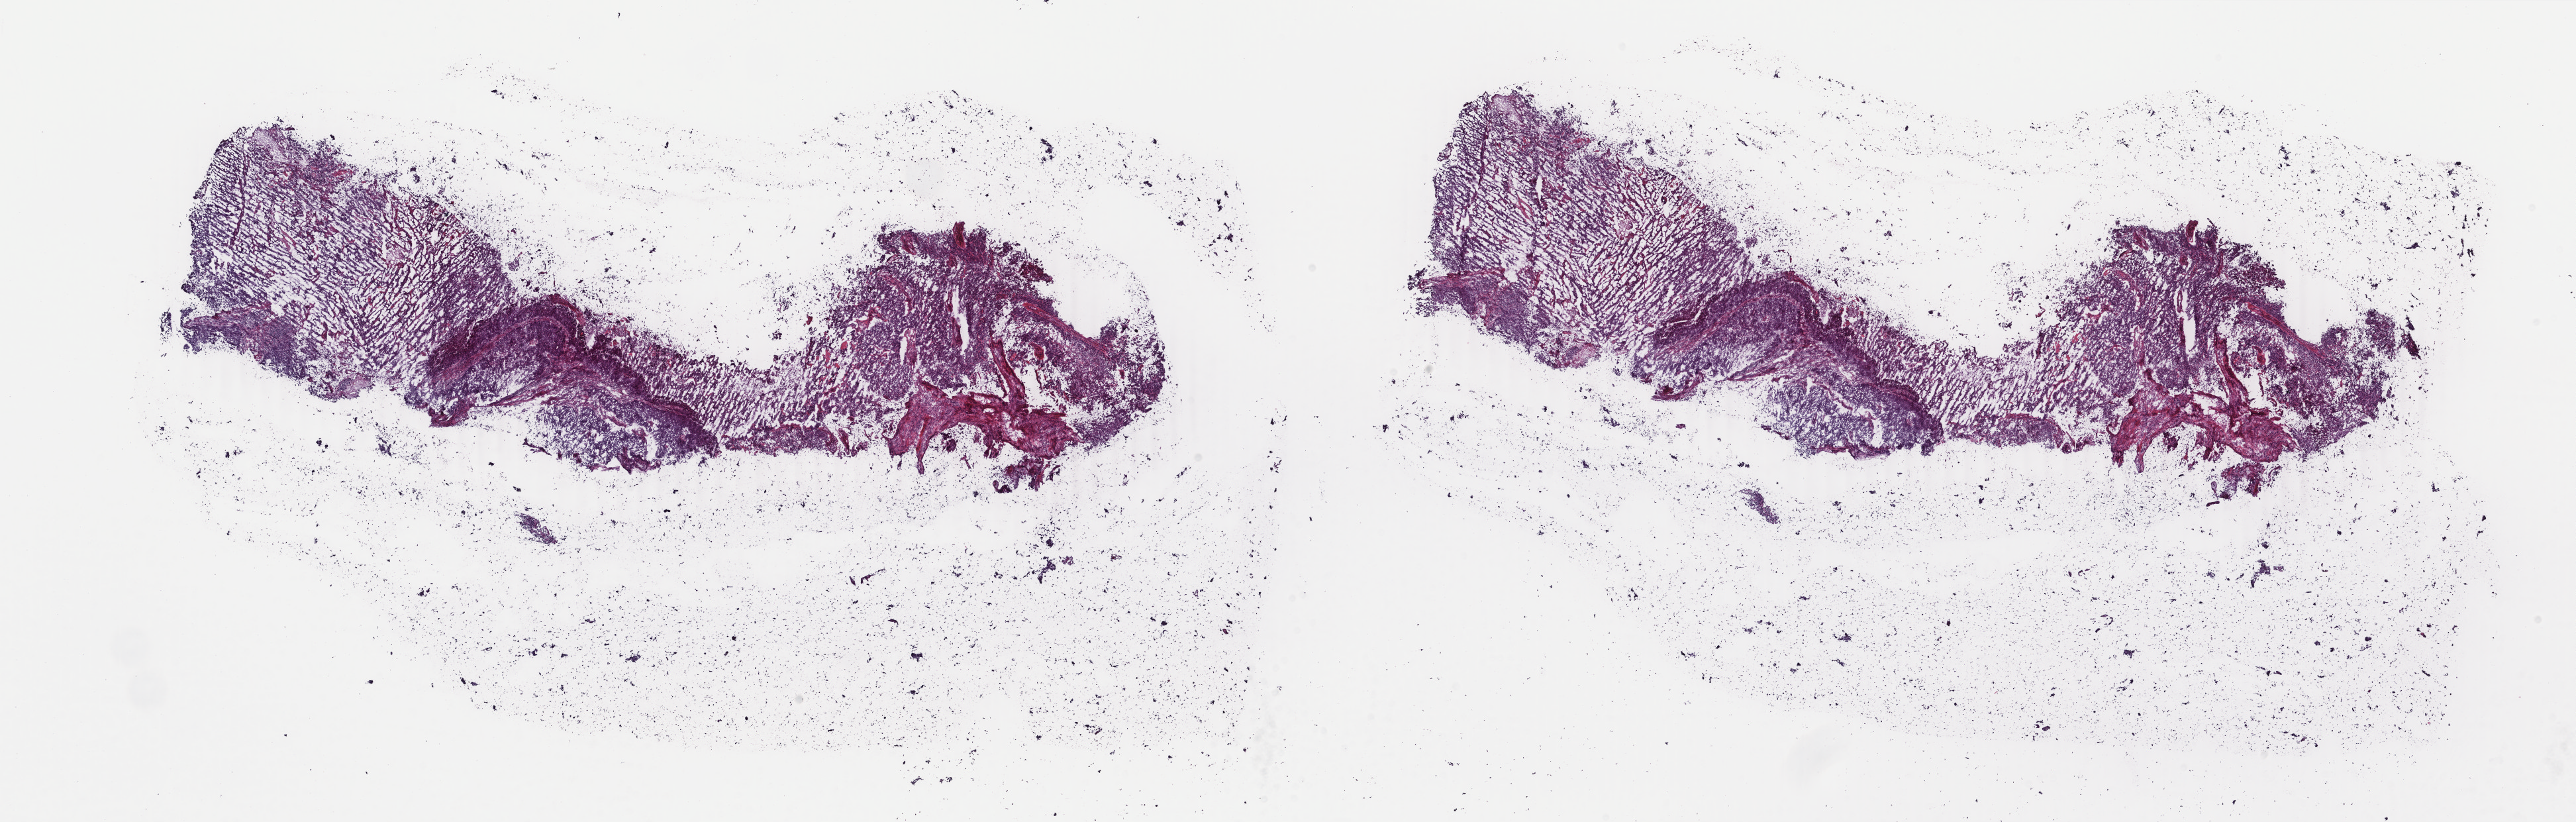
Whole-slide histology image, Hematoxylin and eosin (H&E) stained, shown as a low-resolution overview of the whole scanned area (about 30.9 x 9.9 mm), frozen section from the top of the tissue portion, primary tumour sample from the uterus. Female patient; age at initial diagnosis 51 years. Histologic grade: G3 (poorly differentiated). Slide review estimates, as recorded: tumour cells 66%, tumour nuclei 70%, normal cells 0%, stromal cells 30%, necrosis 4%. Inflammatory infiltration, as recorded: lymphocyte infiltration 8%, monocyte infiltration 3%, neutrophil infiltration 0%.
- FIGO stage: II
- diagnosis: Endometrioid adenocarcinoma, NOS (endometrium)